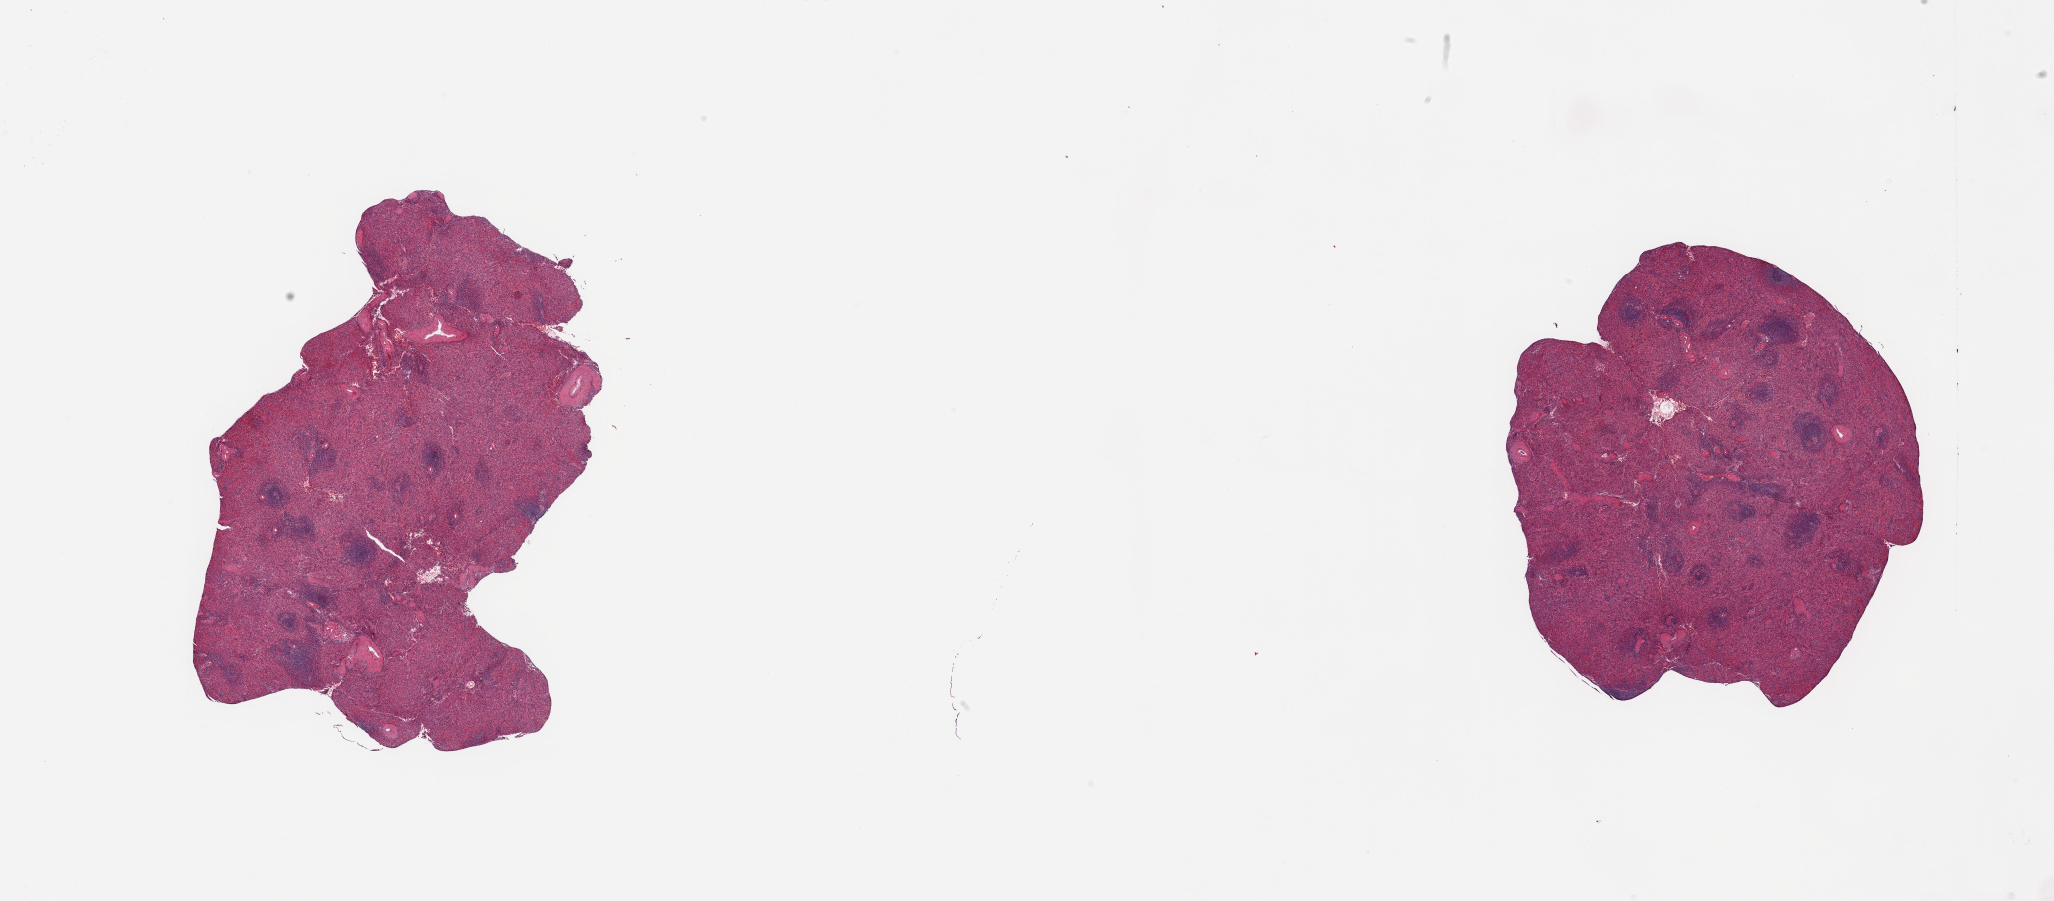
Digitized haematoxylin and eosin-stained section, brightfield, whole scanned area (about 32.5 x 14.3 mm, acquisition: 20x scan) shown as a low-resolution overview, PAXgene-fixed paraffin-embedded (PFPE) section, section of spleen (target tissue), donor tissue sample. Donor sex: male.
Reviewer comment on this tissue sample: 2 pieces.